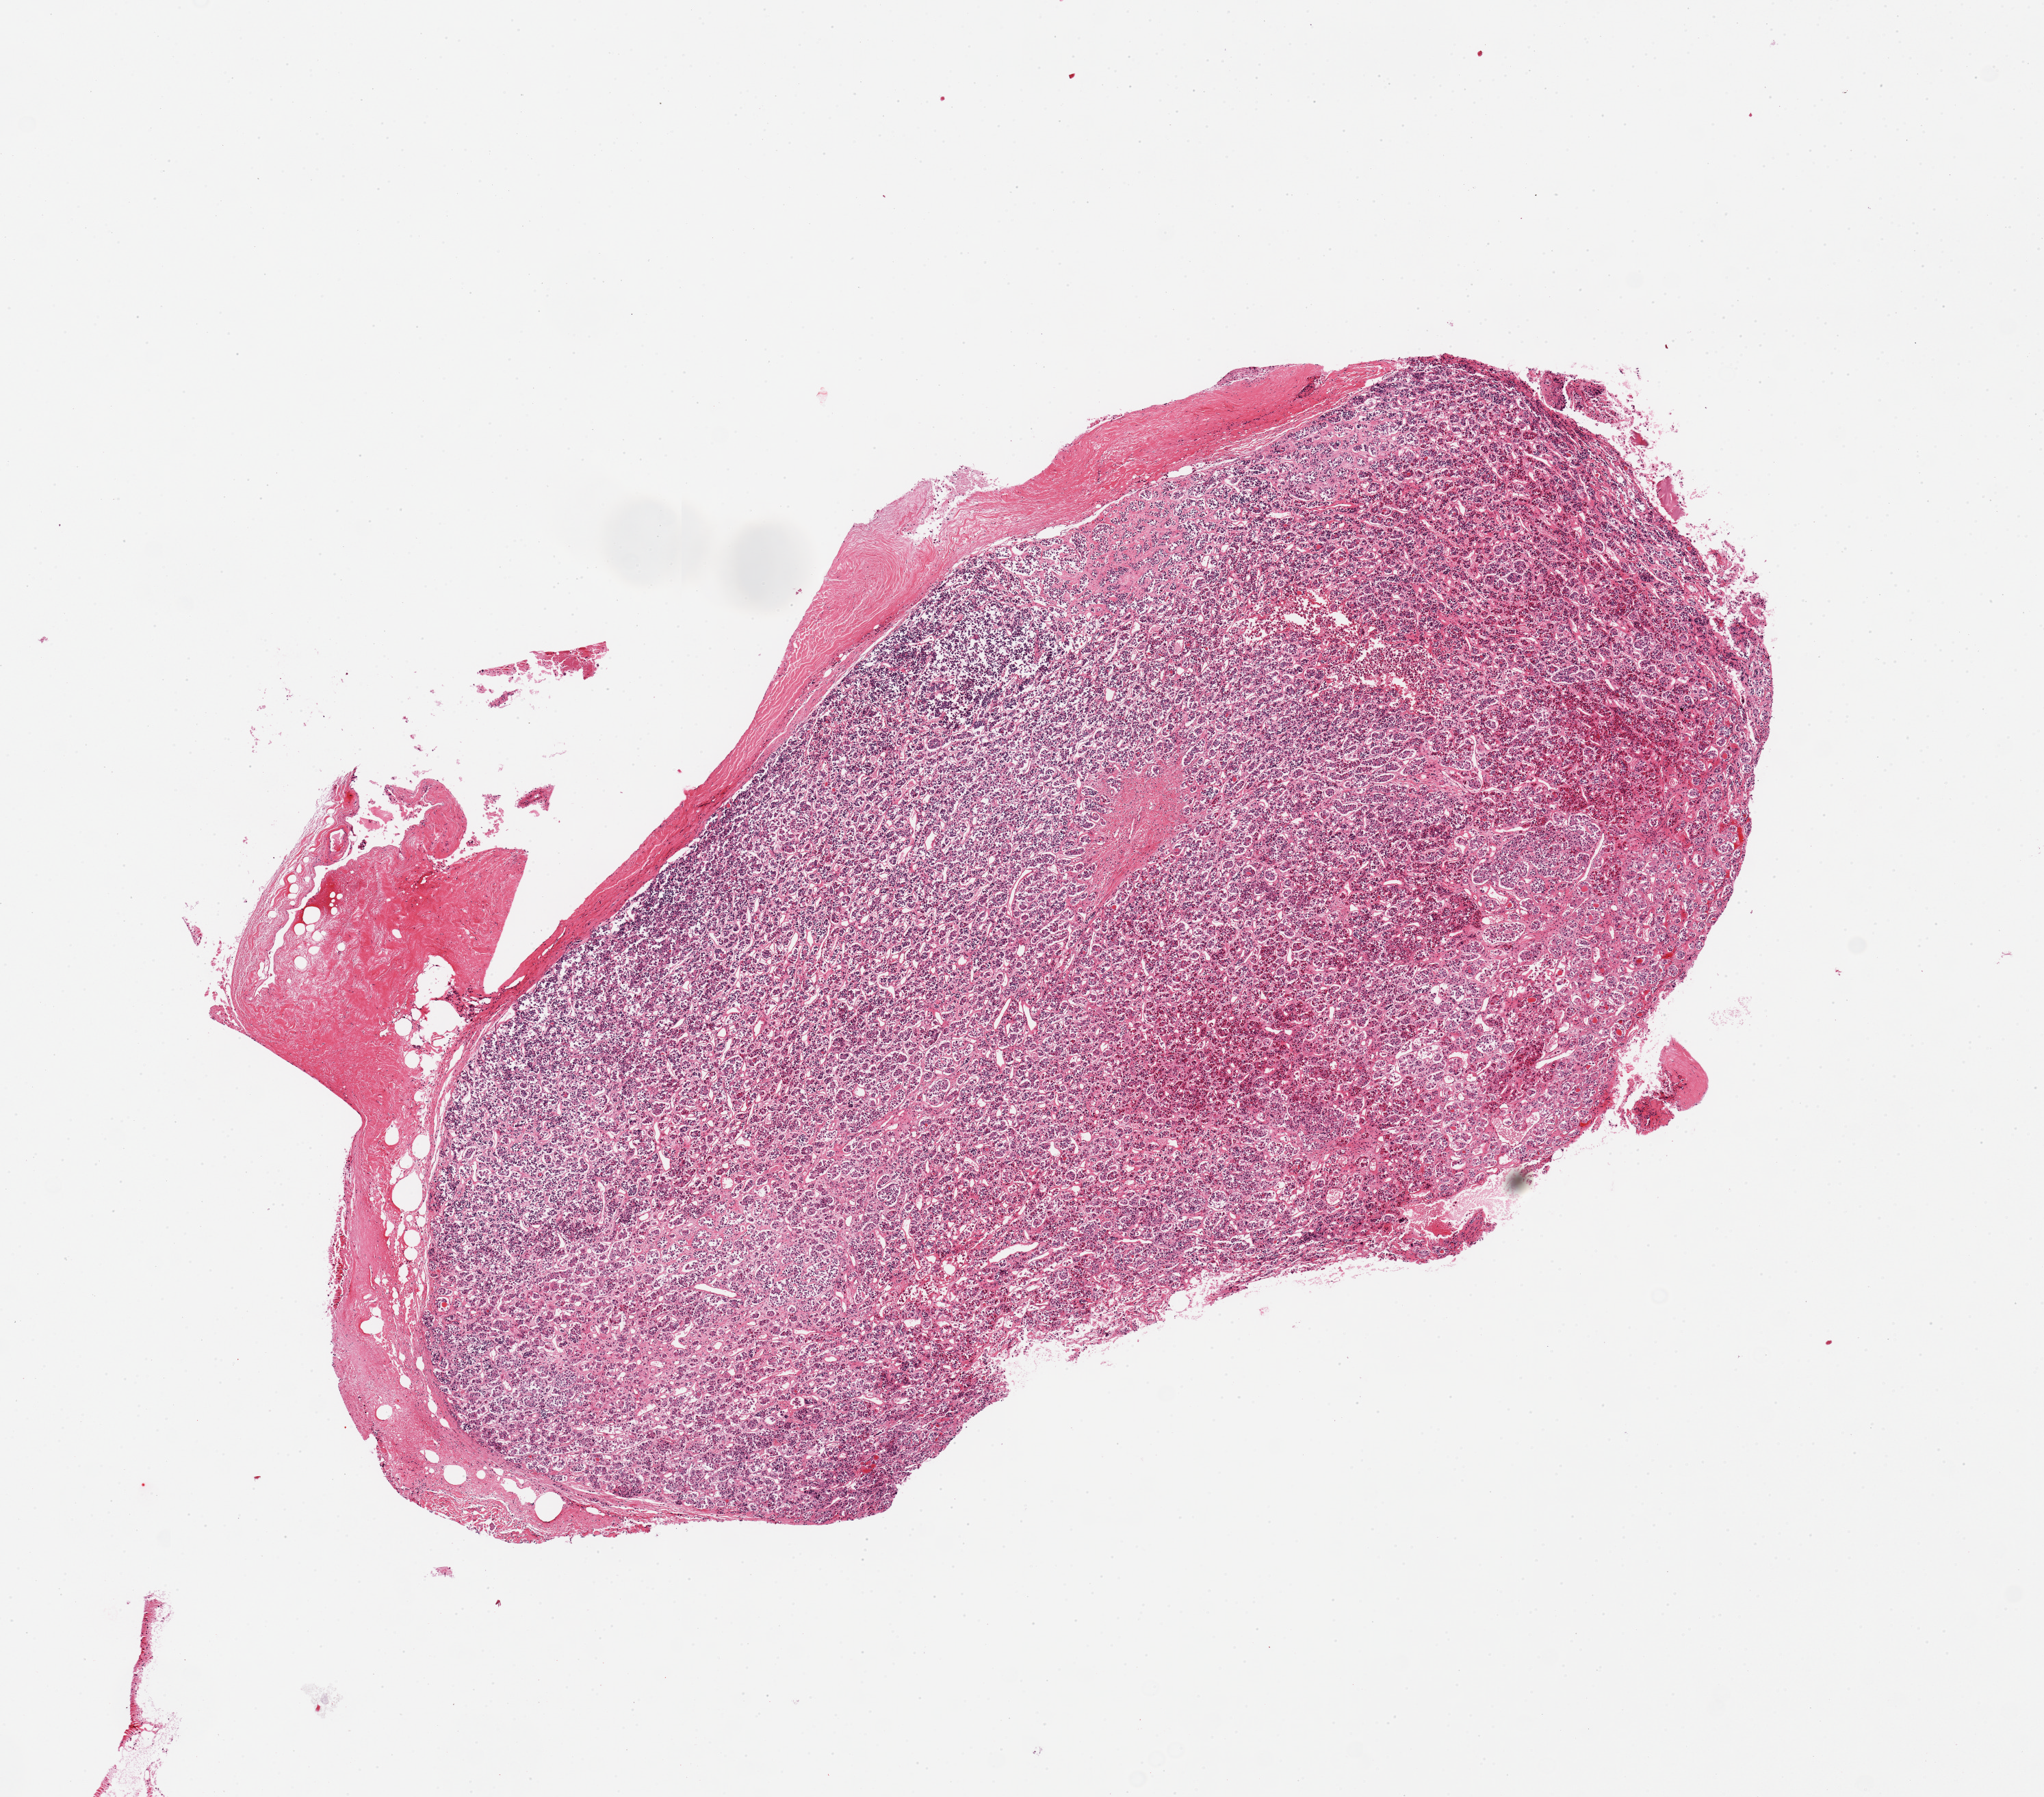
Haematoxylin and eosin whole-slide image — whole scanned area (about 11.8 x 10.4 mm) shown as a low-resolution overview. PAXgene-fixed, paraffin-embedded tissue. Target tissue: pituitary. Donor tissue sample. Female donor.
Reviewer comment on this tissue sample: 1 piece, adenohypophysis.